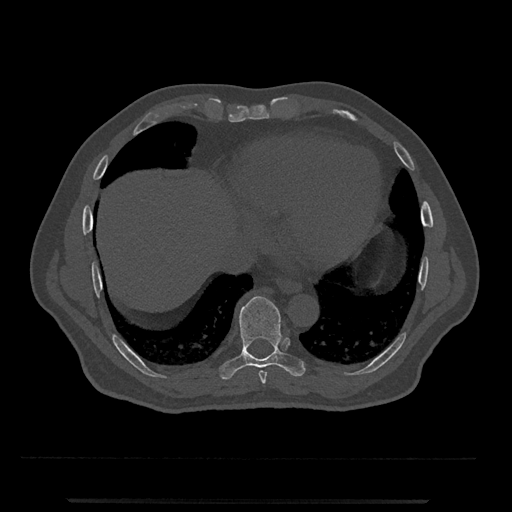
CT including the spine, one axial slice; position 581 of 797 along the scan axis; bone window (W 1800 / L 400 HU); 0.5 mm slice thickness; 512 × 512 image matrix. Patient: male, 63 years. From the clinical record (not read from this slice): primary cancer: prostate.
Outlined on this slice (semi-automatic segmentation, software-assisted and operator-edited):
- T8 vertebra: bounding box (x1, y1, x2, y2) in pixels: (259, 371, 267, 384)
- T9 vertebra: (219, 296, 306, 380)